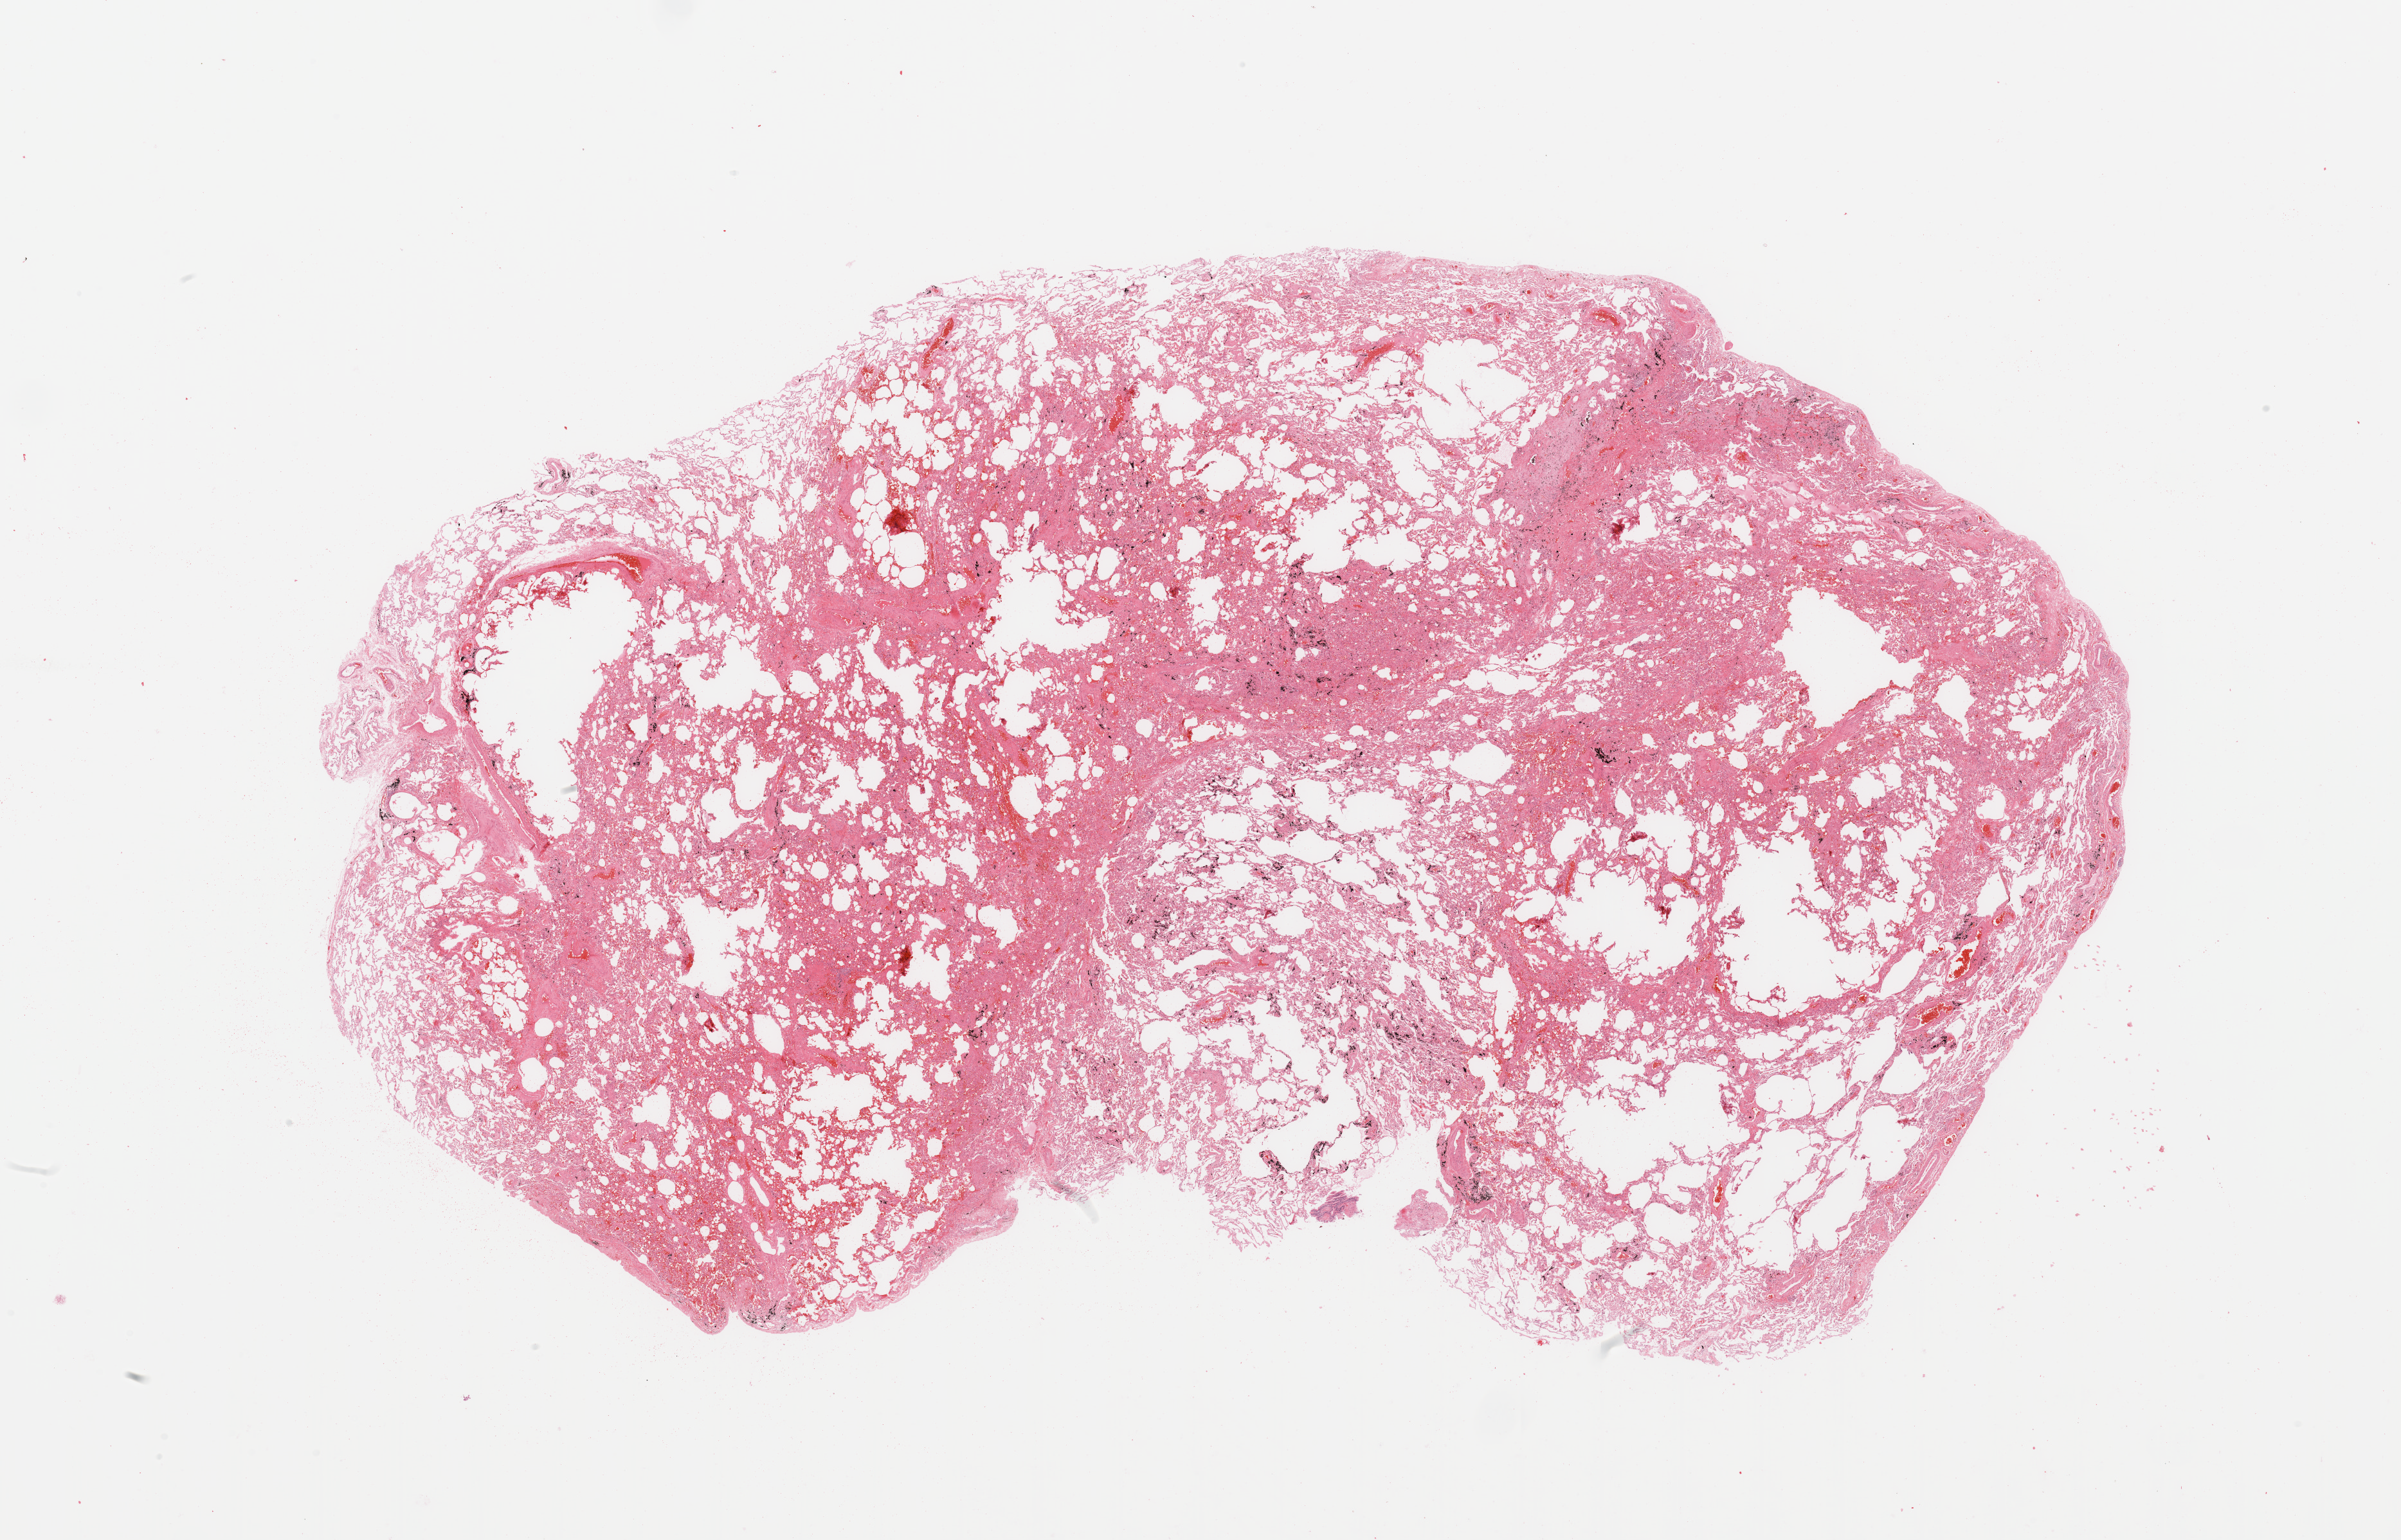
Whole-slide histology image, H&E-stained, low-resolution overview of the scanned area, about 29.5 x 18.9 mm, normal (non-tumour) tissue sample, sampled site: lung. 72-year-old male patient.
This section: normal (non-tumour) tissue from the same patient. Patient diagnosis: Adenocarcinoma, NOS.